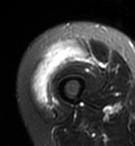
MRI of an extremity soft-tissue mass, one axial slice; position 17 of 95 along the scan axis; T2-weighted fat-saturated; MR volume resampled by the dataset authors to the PET/CT grid (not the native acquisition matrix); 3.27 mm slice thickness; 135 × 146 image matrix, field of view 132 × 143 mm. Female patient. From the clinical record (not read from this slice): histological type: pleiomorphic undifferentiated sarcoma; grade: high; site of the primary tumour: right quadricep.
Structures marked on this image (expert contour drawn on MRI and transferred to this co-registered scan by the dataset authors):
- gross tumour volume including surrounding oedema: bounding box [x1, y1, x2, y2] px = [32, 41, 86, 103]